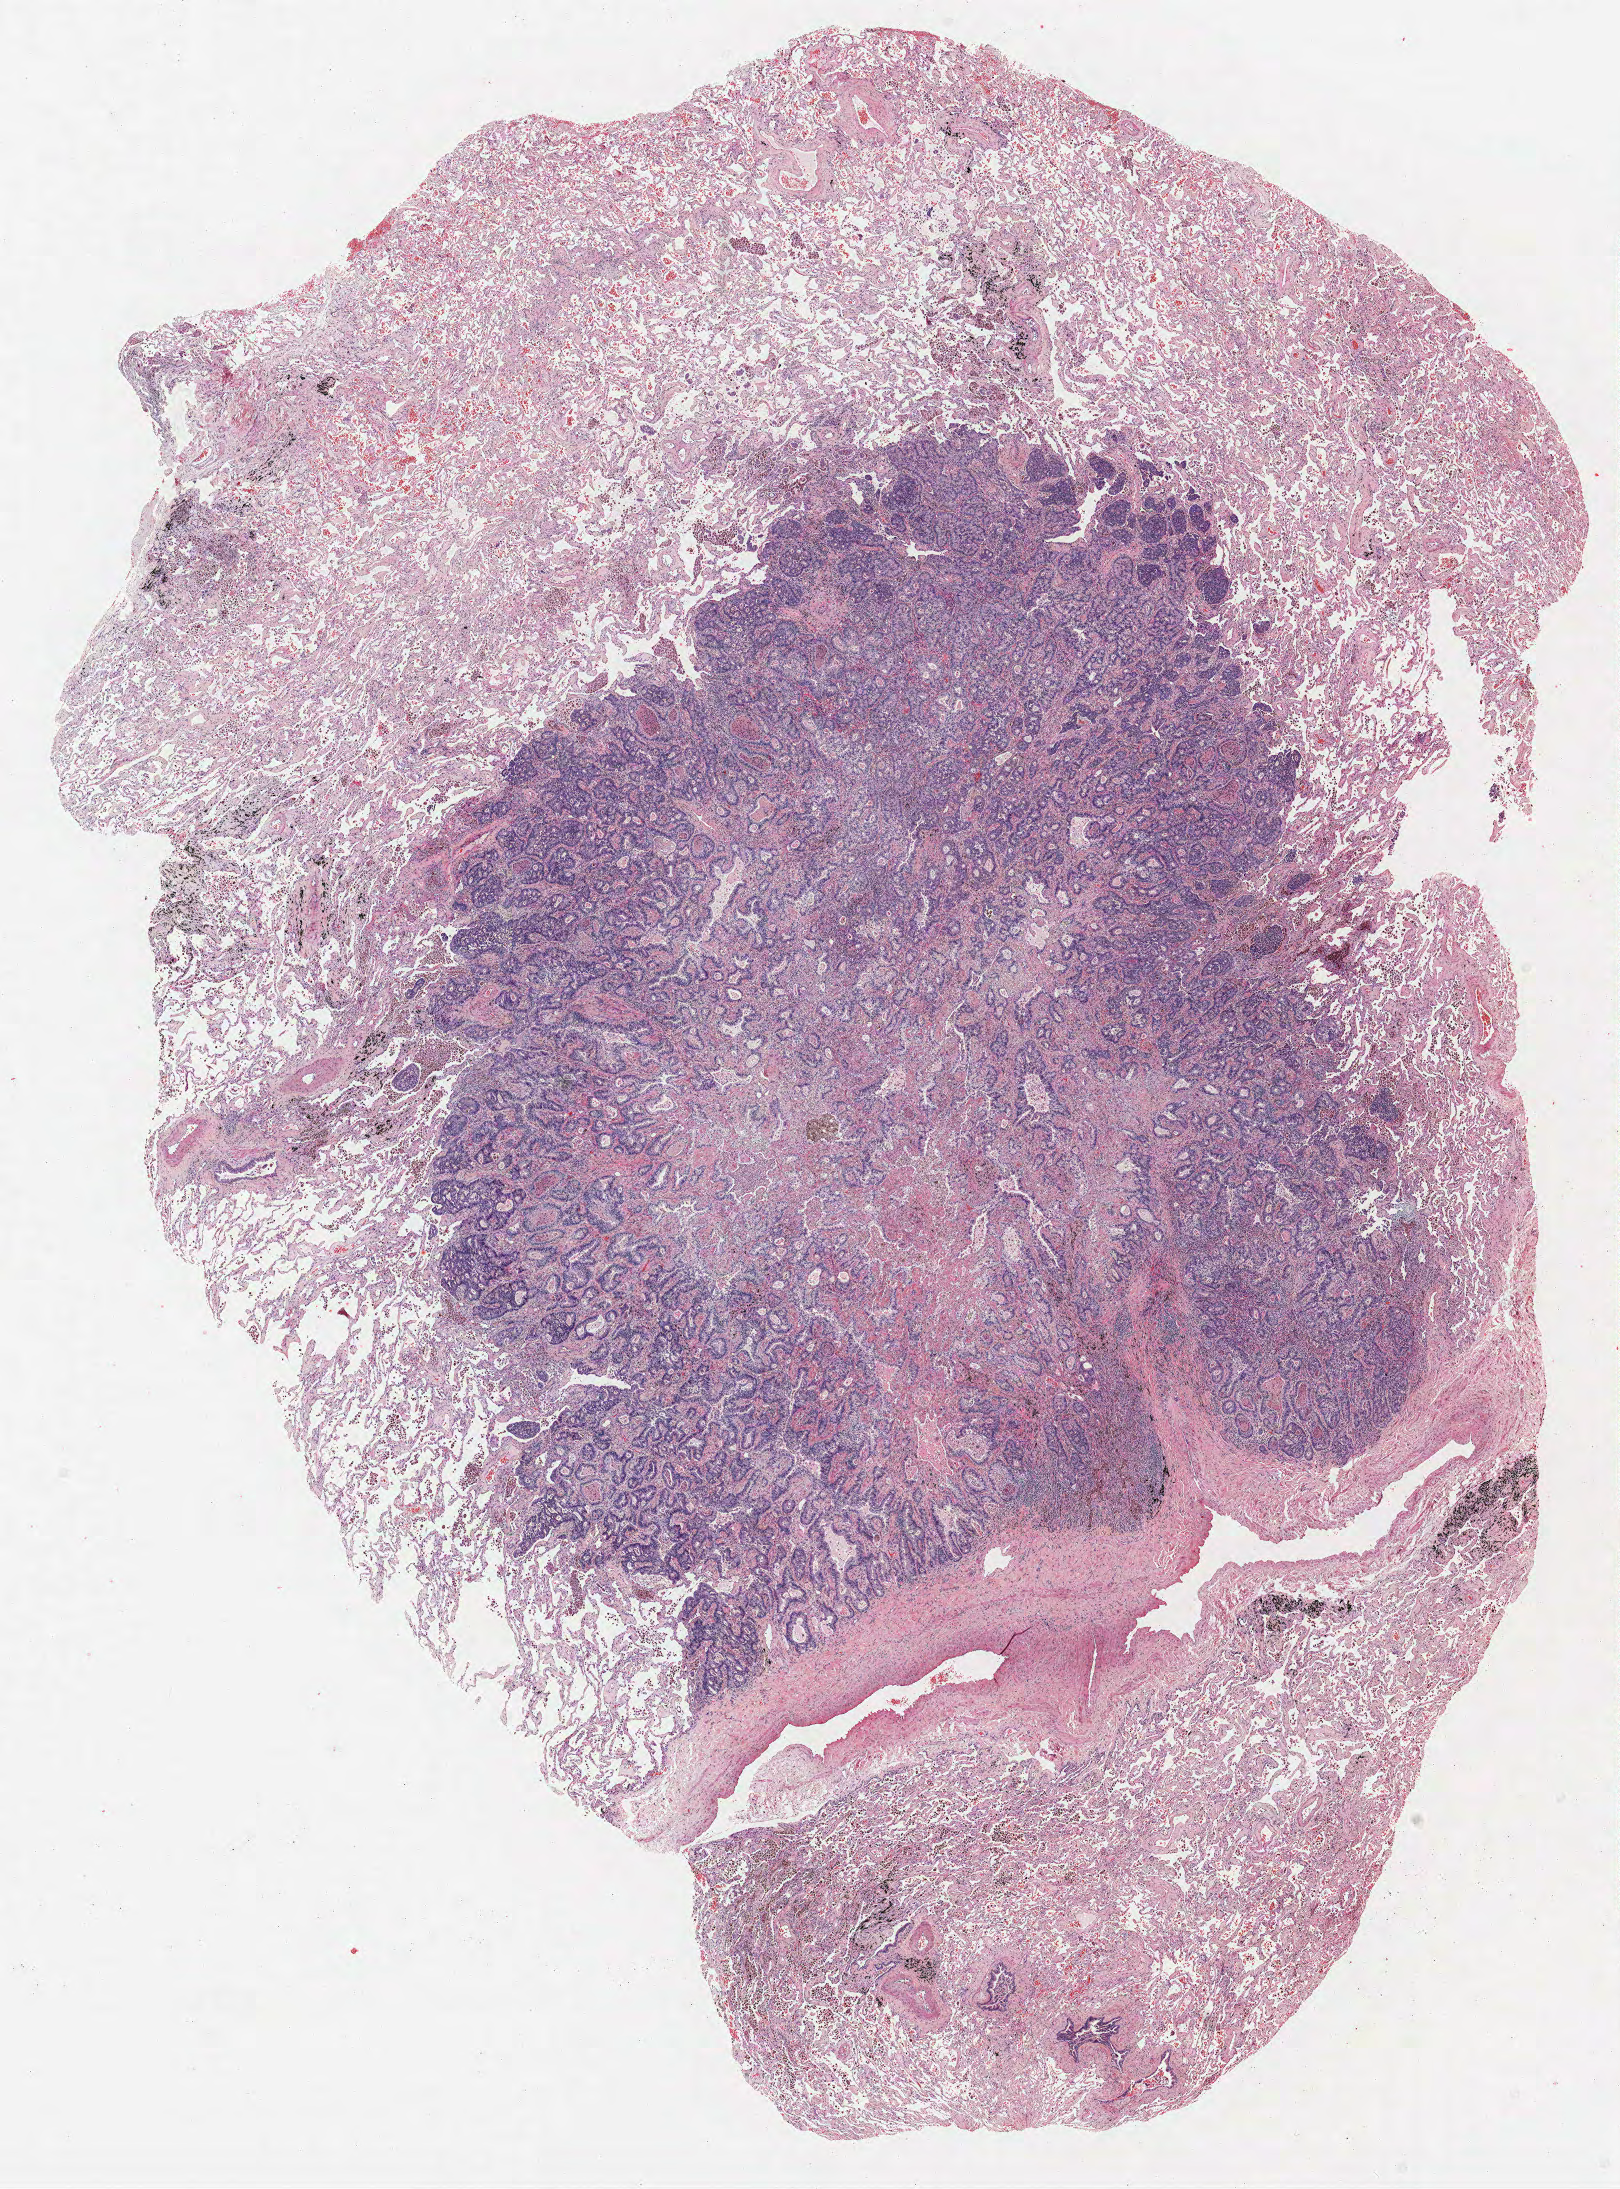
Whole-slide histology image, Hematoxylin and eosin (H&E) stained — a low-resolution overview of the entire scanned area, about 13.0 x 17.5 mm; FFPE section; lung tissue. Male patient, aged 69 at enrolment. Former smoker at enrolment. Grade: well differentiated (G1).
Participant's lung-cancer diagnosis: Adenocarcinoma, NOS. Tumour size (pathology): 17 mm. Primary tumour location (clinical record): right upper lobe. Stage (AJCC 6th edition): IA. ICD-O-3 topography: upper lobe of lung (C34.1).